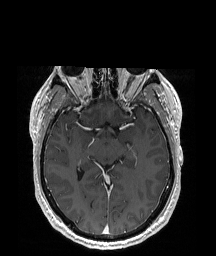
Brain MRI from a brain-tumour surgery series, one axial slice. Slice 112 of 192 in the series (ordered by position). T1-weighted post-contrast. 216 × 256 image matrix. Case-level facts recorded for this patient, not image findings: histopathology: Glioblastoma; WHO grade: 4; IDH mutation: no; tumour location: Left Temporal Parietal.
Annotated regions visible in this slice (outlined manually by an expert reader):
- tumour: bounding box (x1, y1, x2, y2) in pixels: (156, 190, 161, 195)